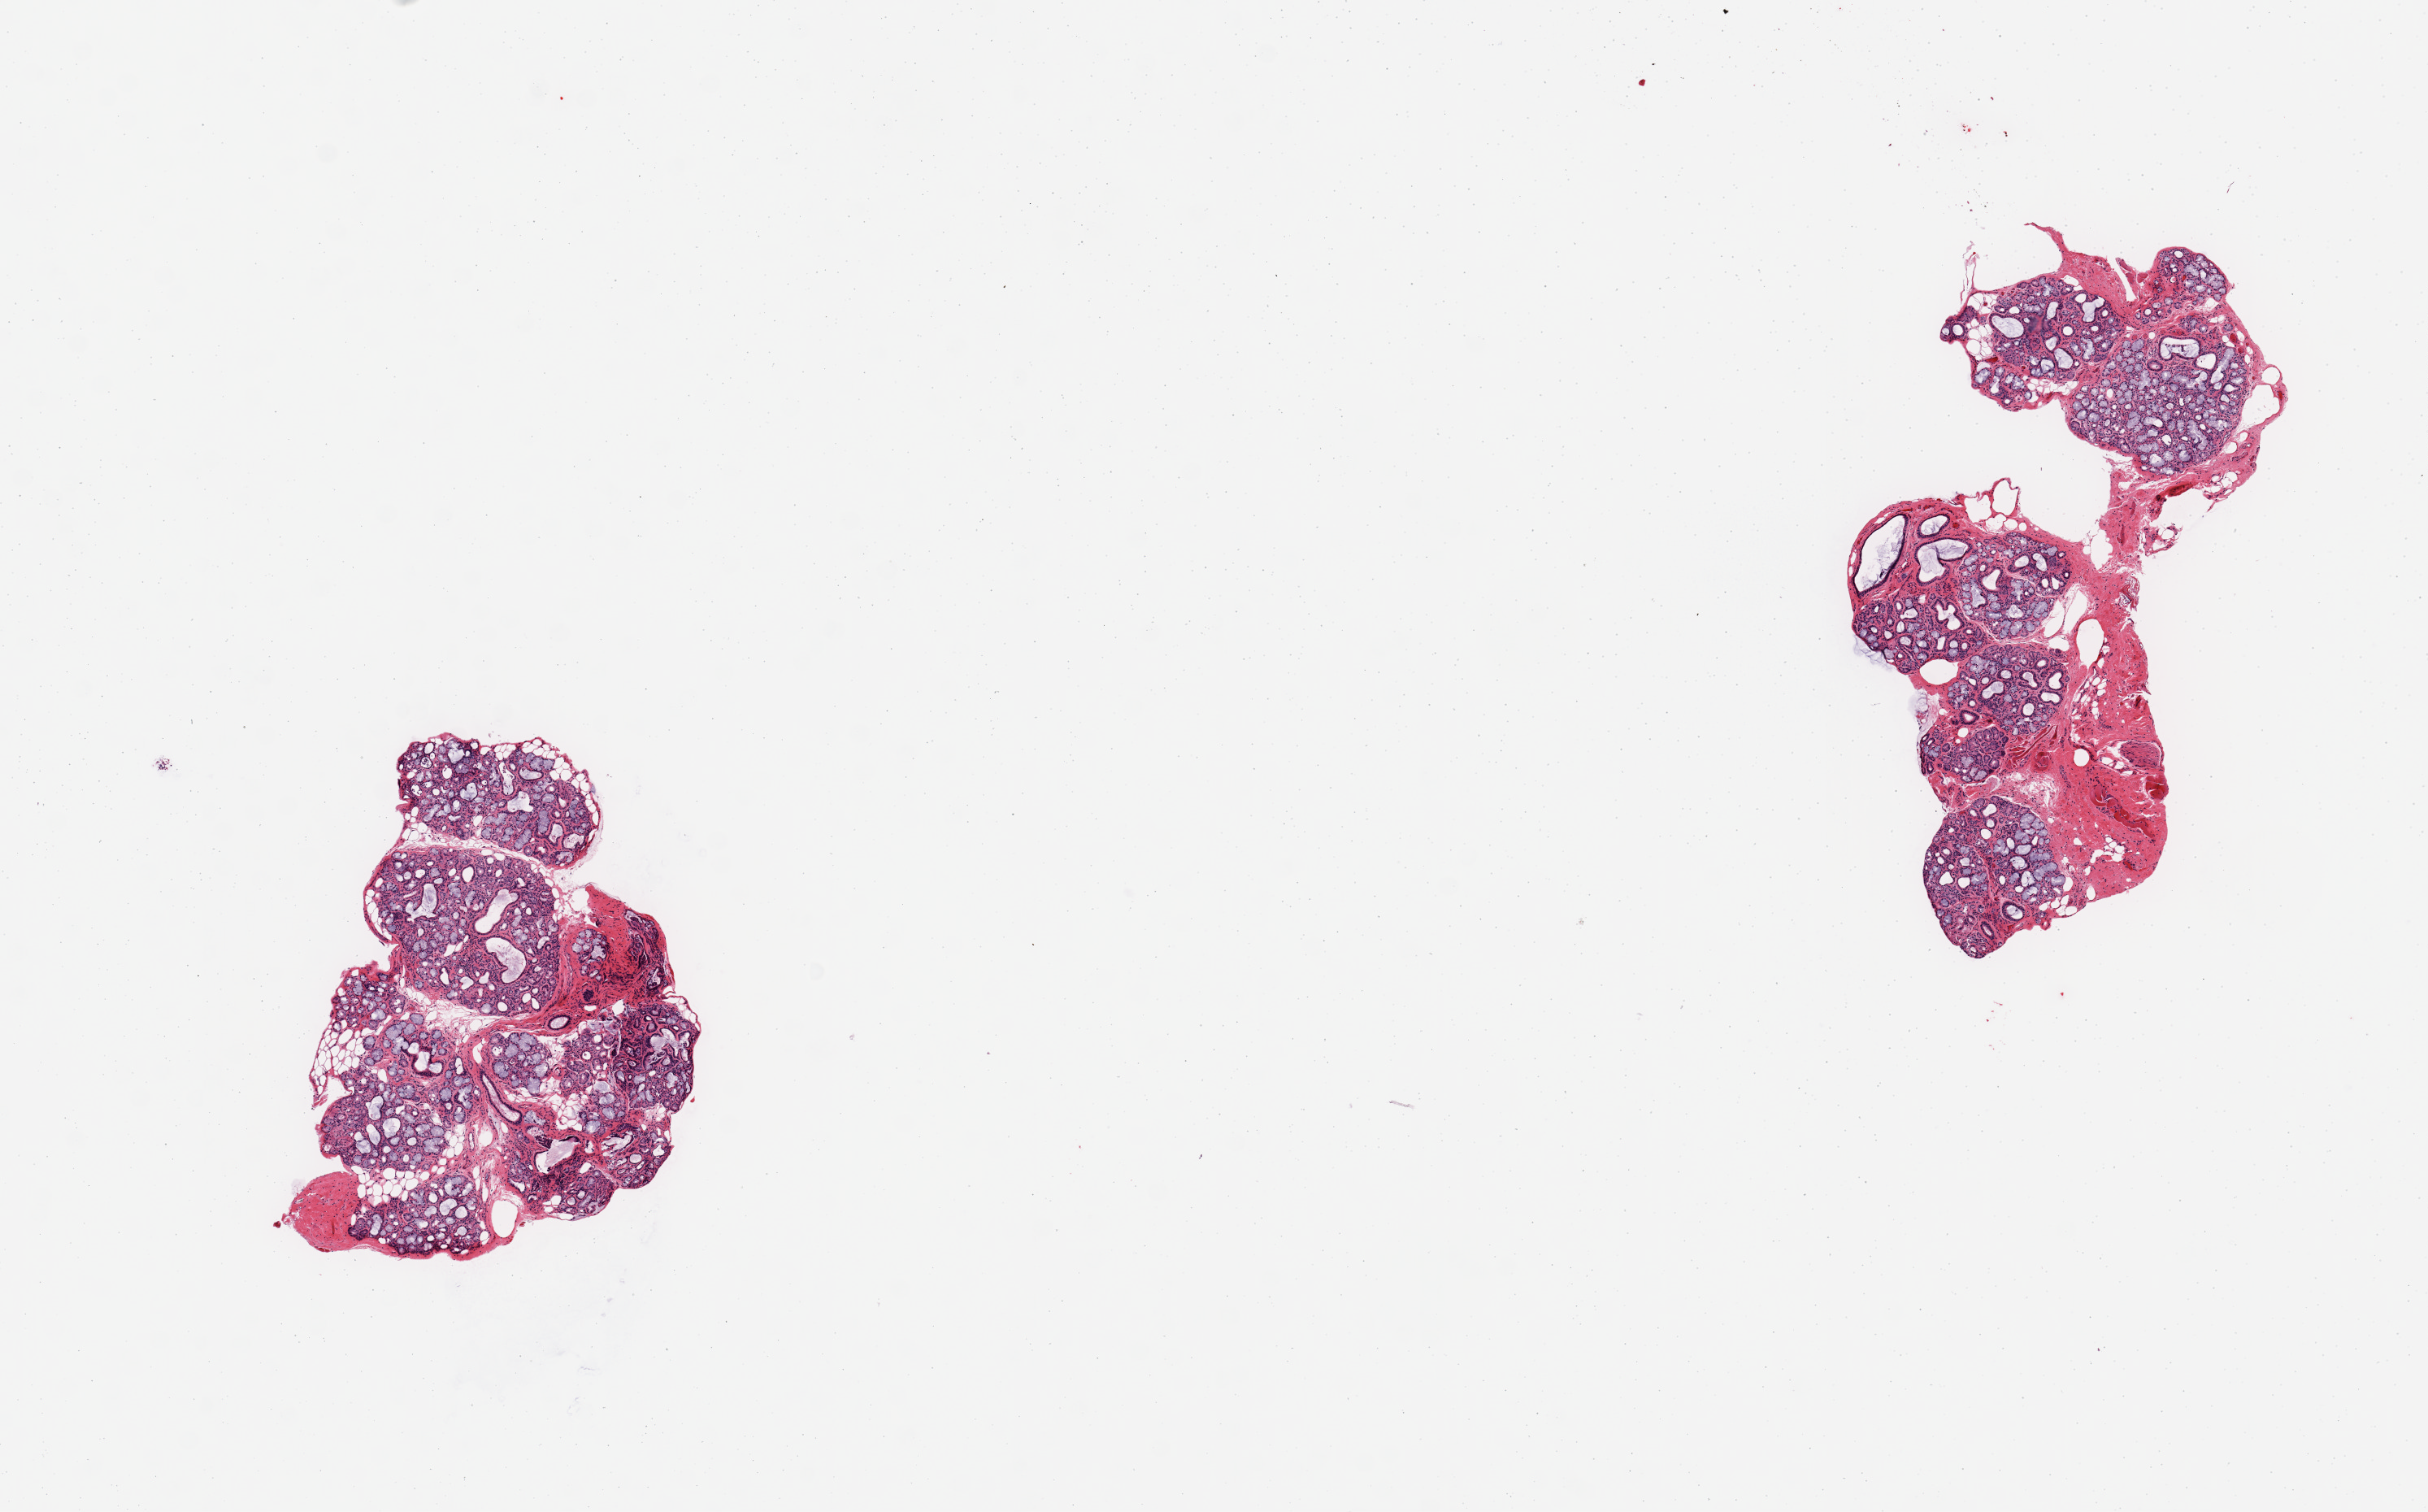
Whole-slide image, haematoxylin and eosin stain, a low-resolution overview of the entire scanned area, about 11.8 x 7.4 mm, PAXgene-fixed paraffin-embedded (PFPE) section, target tissue: minor salivary gland, donor tissue sample. Donor: male.
Review note (as recorded): 2 pieces; well dissected salivary glands.